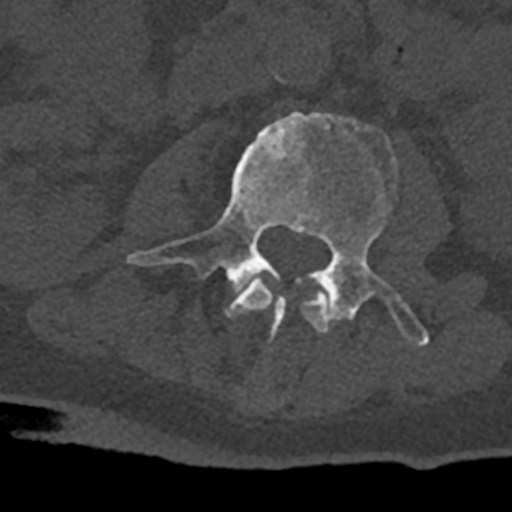
CT including the spine, one axial slice. Position 331 of 797 along the scan axis. Reconstruction kernel Br40s/3. 120 kVp. Bone window (W 1800 / L 400 HU). 0.5 mm slice thickness. 512 × 512 image matrix, field of view 160 × 160 mm. Patient: male, 74 years. Case-level facts recorded for this patient, not image findings: primary cancer: renal; vertebrae with lytic lesions (as recorded): T10, L1, L2, L3, L4, L5.
Outlined on this slice (semi-automatic segmentation, software-assisted and operator-edited):
- L2 vertebra: box from (x=226, y=279) to (x=329, y=333) px
- L3 vertebra: (x=127, y=112)–(x=429, y=347)